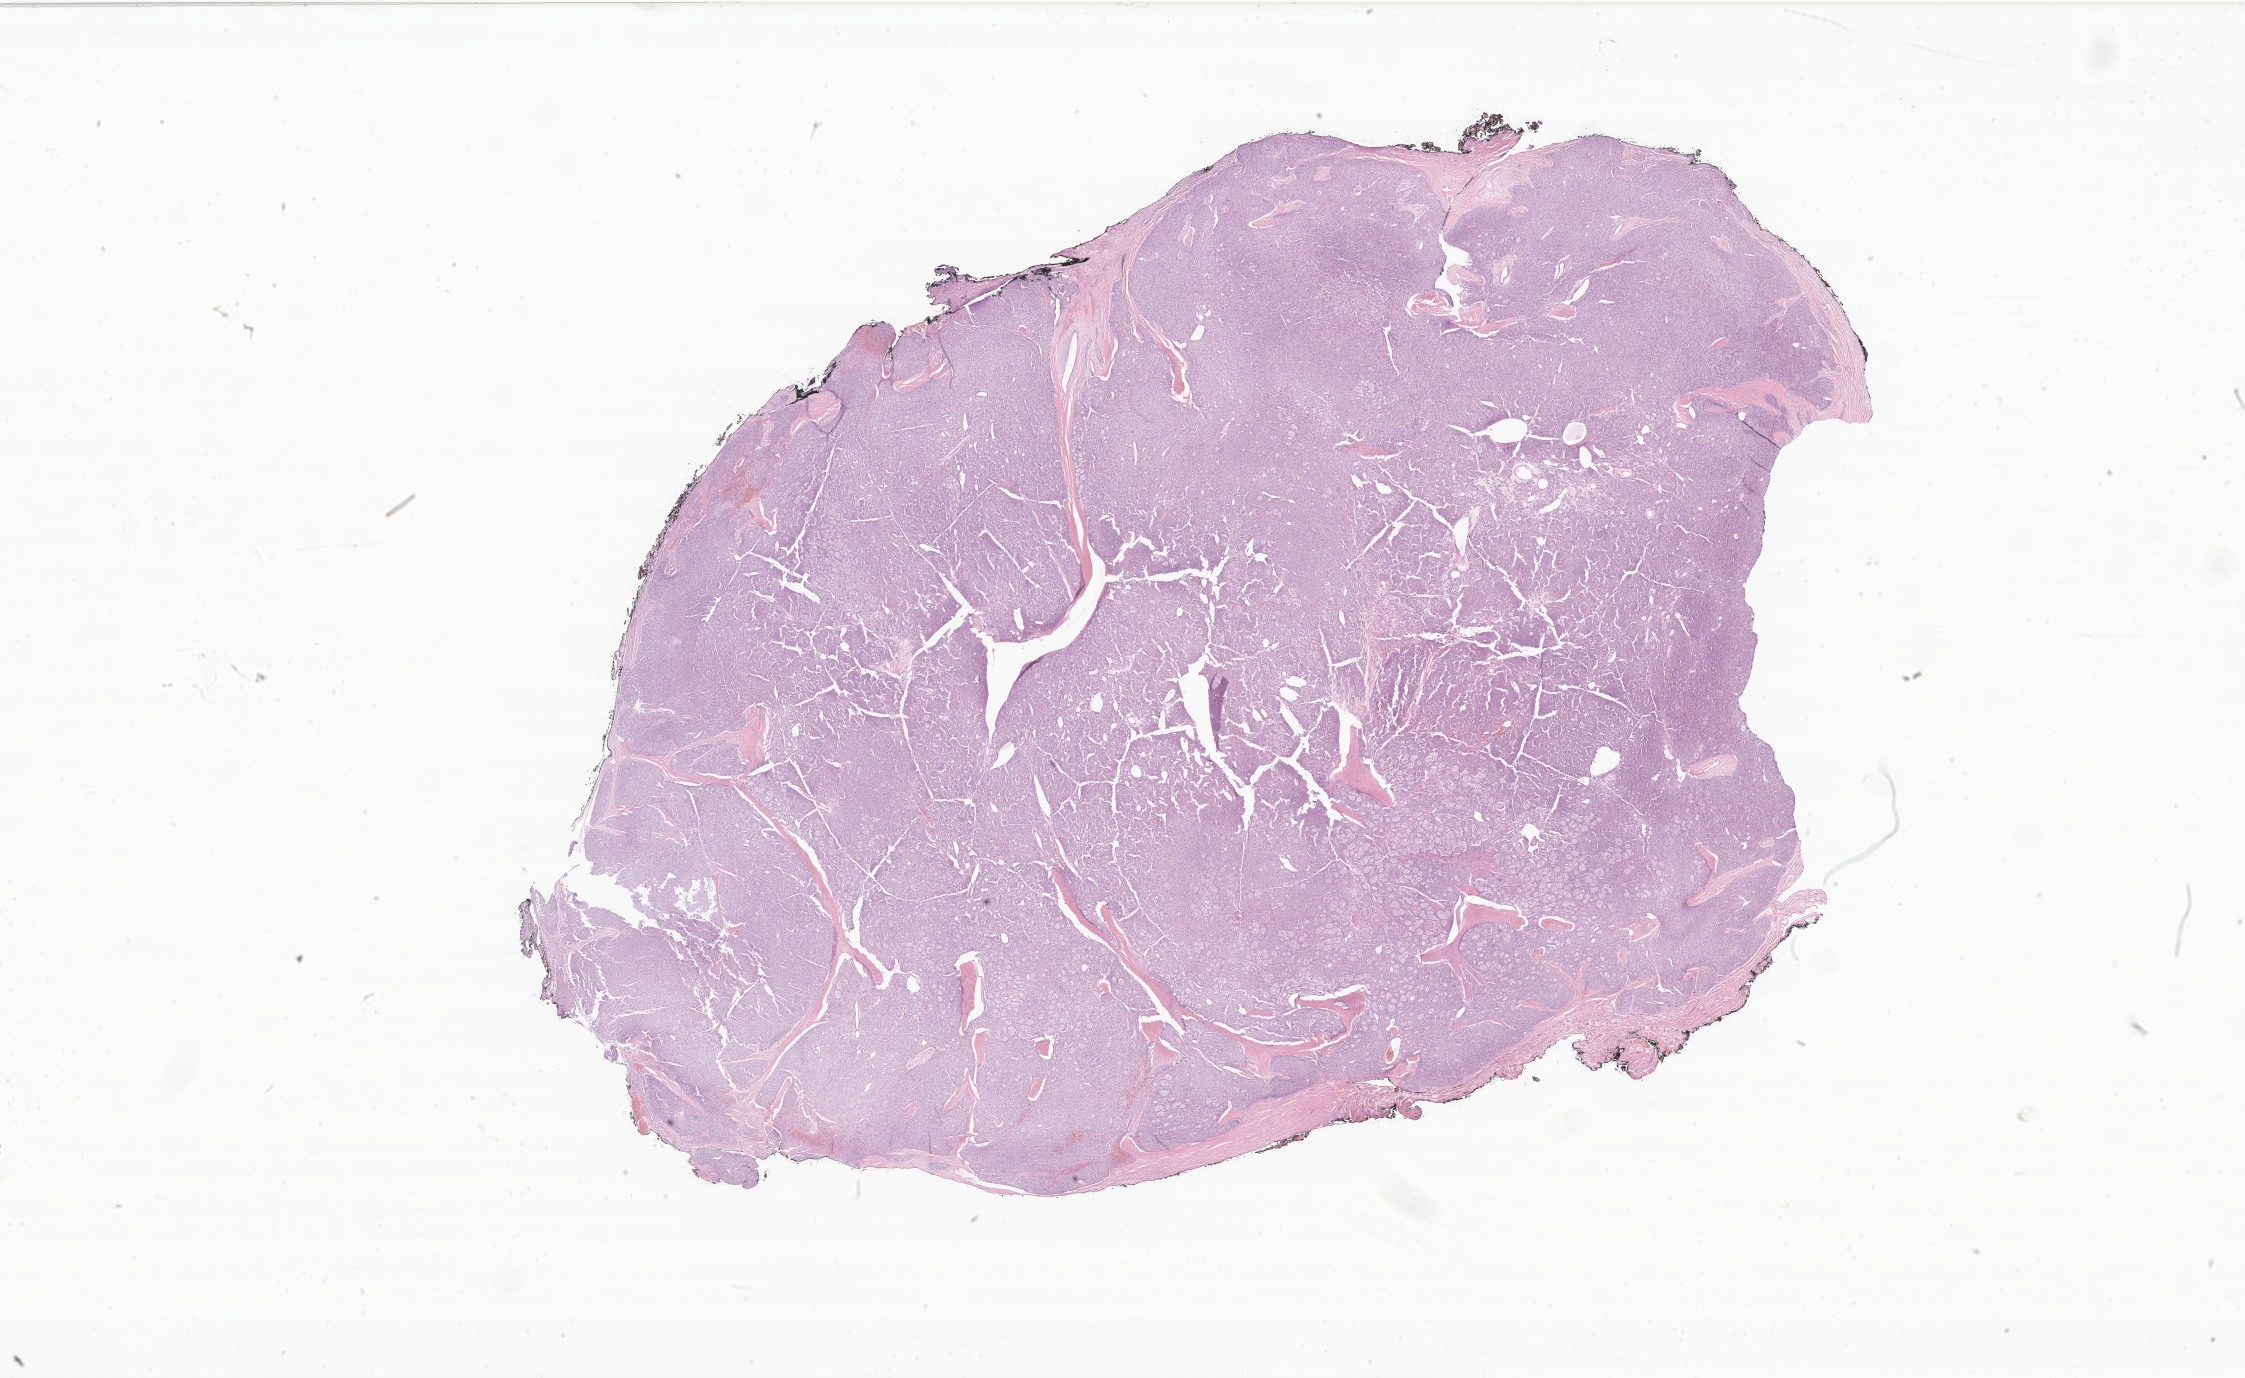
H&E whole-slide image of tumor tissue from the parotid gland — low-resolution overview of the scanned area, about 37.9 x 23.2 mm. Formalin-fixed paraffin-embedded section. Male patient, age 97 months (8 years 1 month).
Diagnosis (ICD-O-3 morphology term): Acinar cell carcinoma.